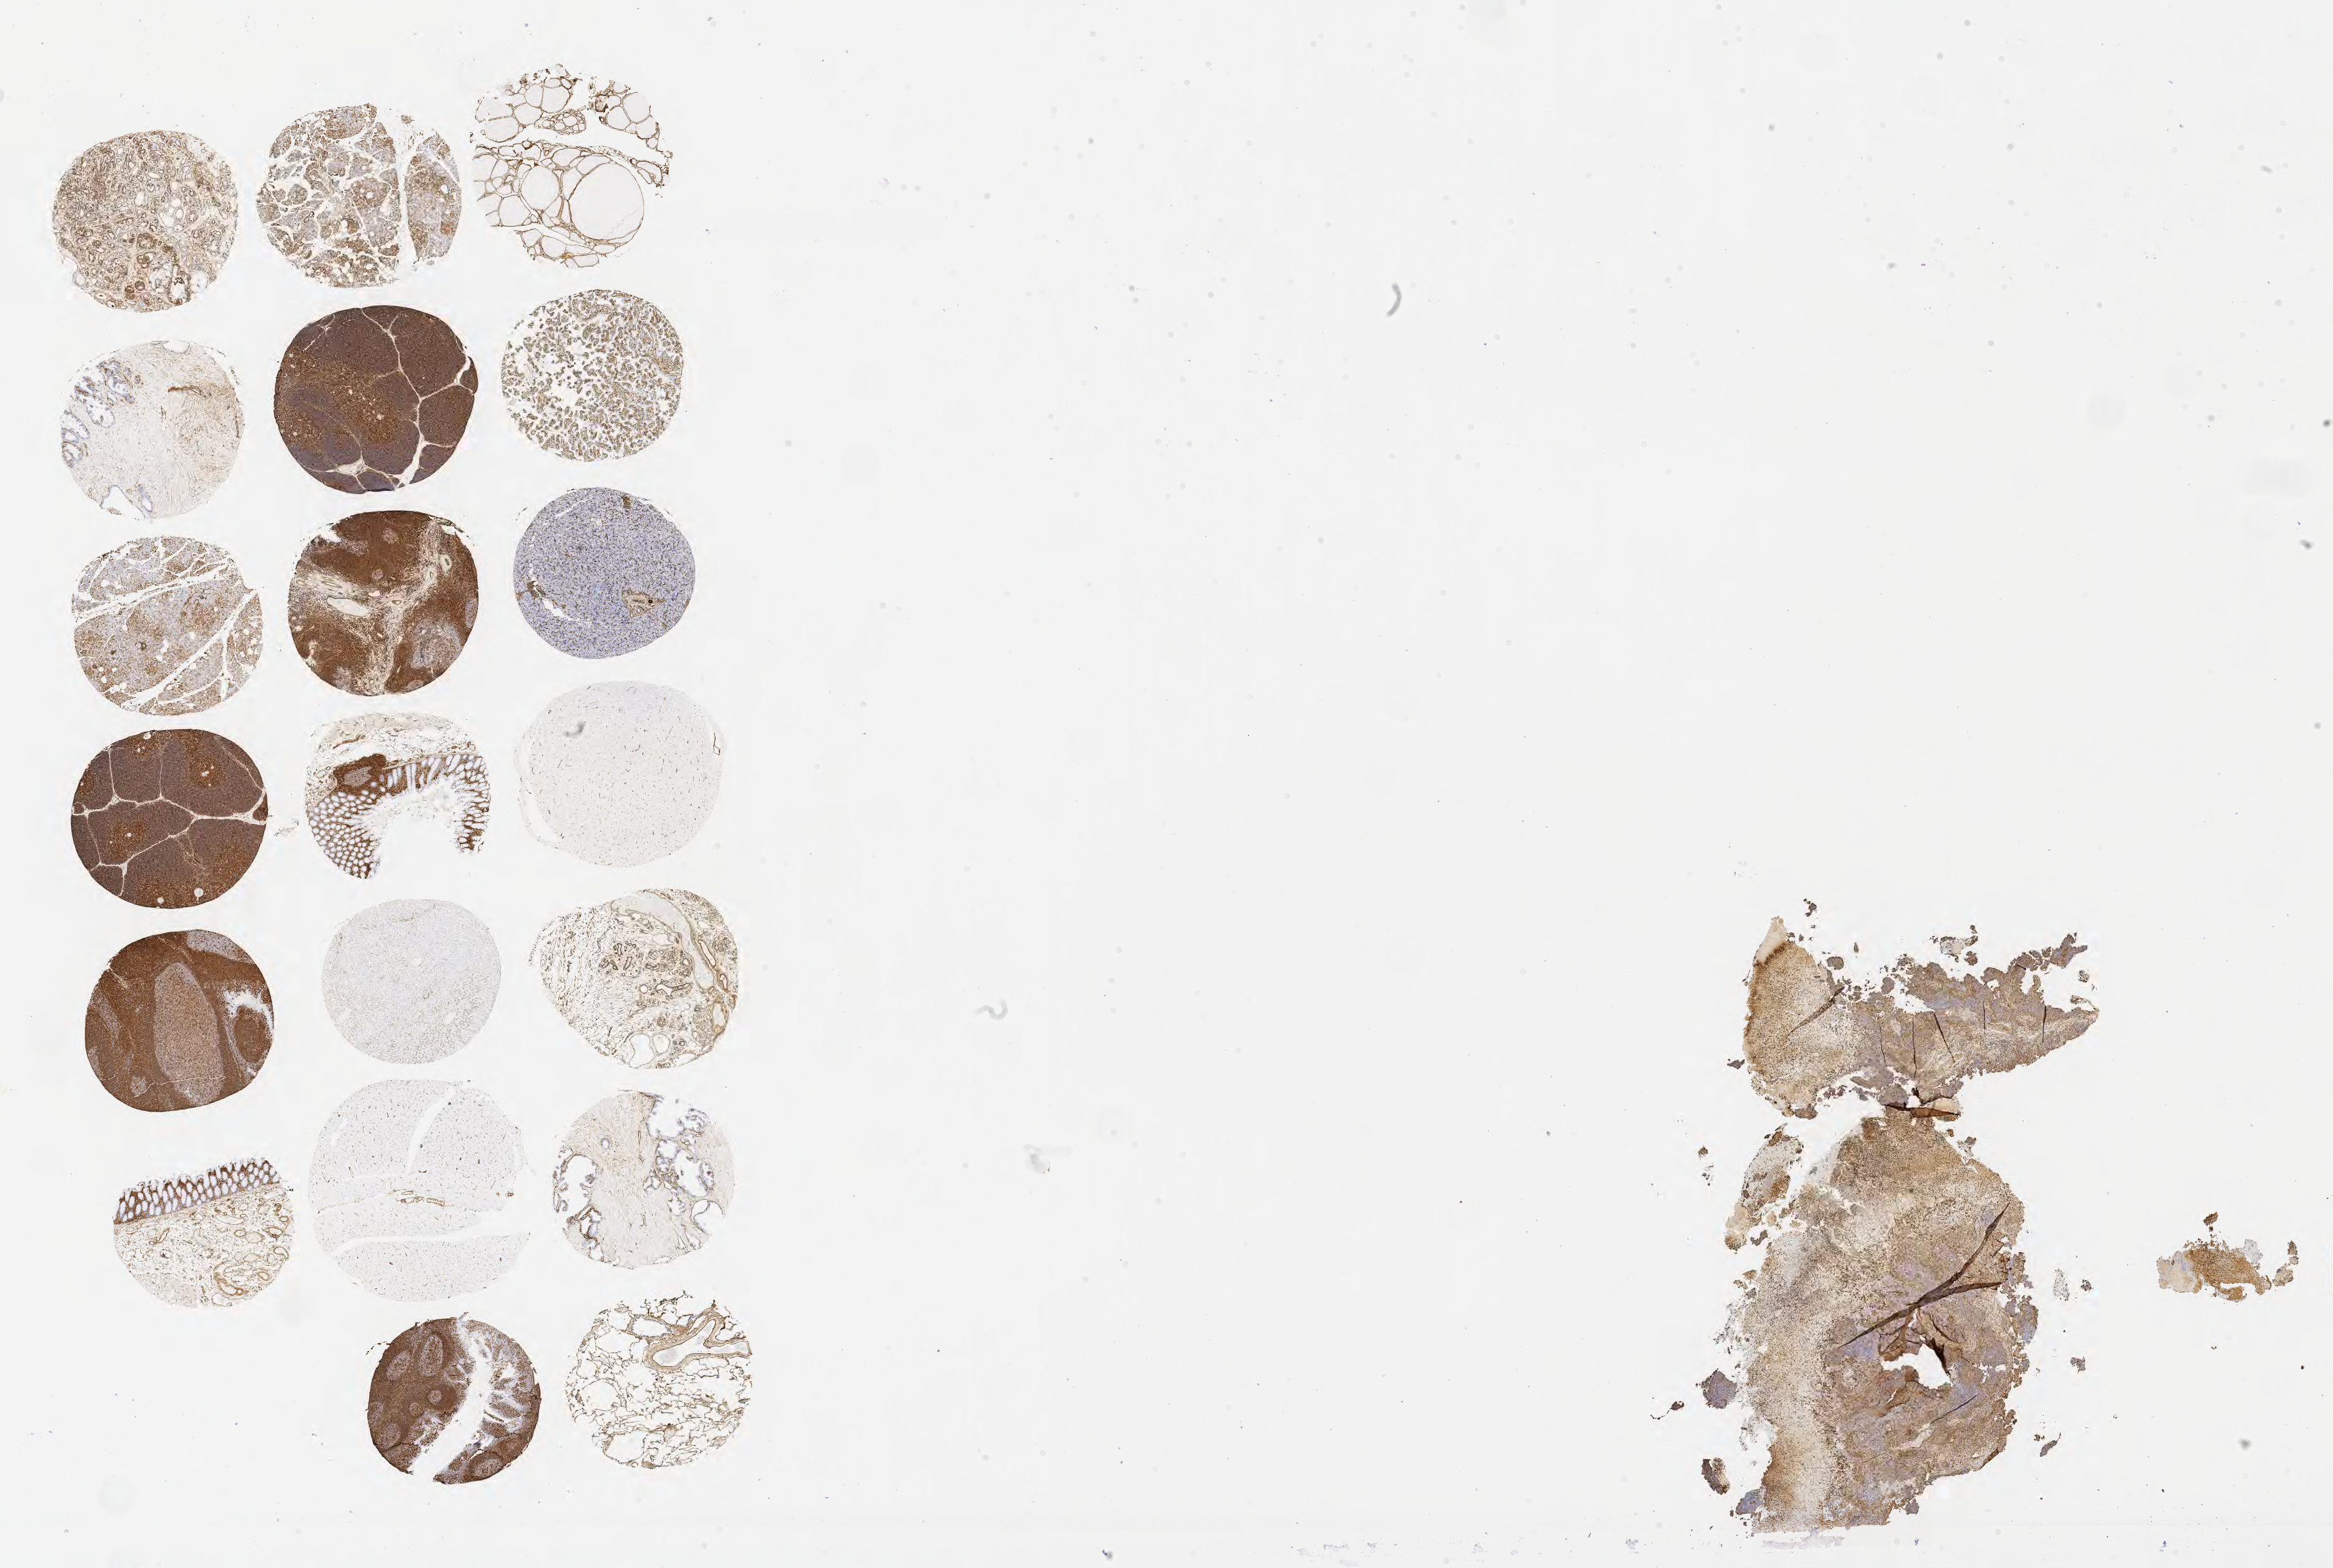
Whole-slide image, immunohistochemical stain for vimentin — a low-resolution overview of the entire scanned area, about 30.2 x 20.3 mm; specimen: tumor tissue; anatomic site: cervix. Patient female; 65 years old.
Histologic diagnosis: Squamous cell carcinoma, large cell, nonkeratinizing, NOS.